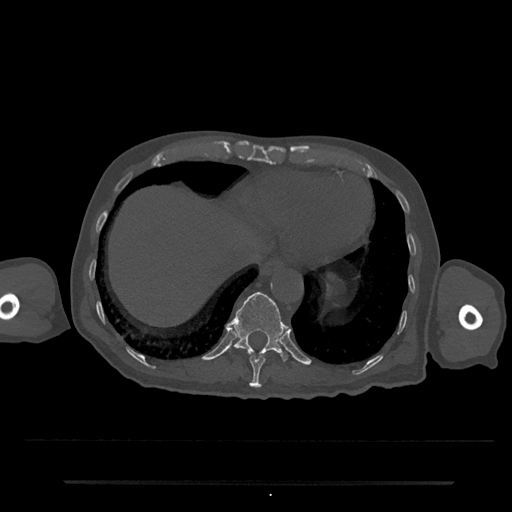
CT including the spine, one axial slice. Position 278 of 797 along the scan axis. Reconstruction kernel Br40s/3. Bone window (W 1800 / L 400 HU). 0.5 mm slice thickness. 512 × 512 image matrix, field of view 427 × 427 mm. Male patient, age 74 years. Case-level facts recorded for this patient, not image findings: primary cancer: prostate.
Structures marked on this image (semi-automatic segmentation, software-assisted and operator-edited):
- T10 vertebra: bounding box [x1, y1, x2, y2] px = [247, 352, 266, 388]
- T11 vertebra: [227, 292, 289, 361]